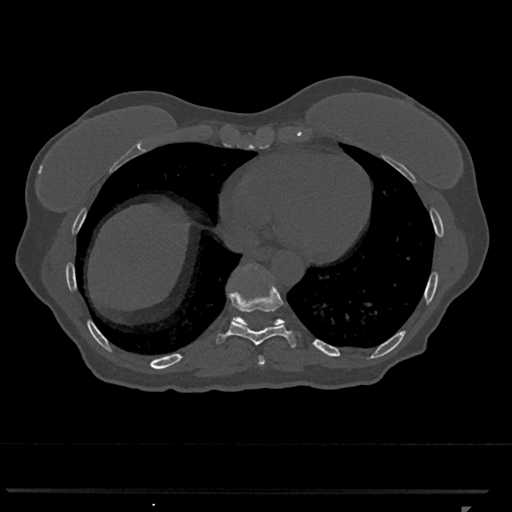
CT including the spine, one axial slice. Position 610 of 793 along the scan axis. Reconstruction kernel Br40s/3. 120 kVp. Bone window (W 1800 / L 400 HU). 0.5 mm slice thickness. 512 × 512 image matrix, field of view 380 × 380 mm. Female patient, age 62 years. From the clinical record (not read from this slice): primary cancer: renal.
Annotated regions visible in this slice (semi-automatically segmented with operator editing):
- T10 vertebra: box from (x=233, y=264) to (x=285, y=327) px
- T8 vertebra: (x=258, y=356)–(x=265, y=365)
- T9 vertebra: (x=217, y=277)–(x=296, y=348)